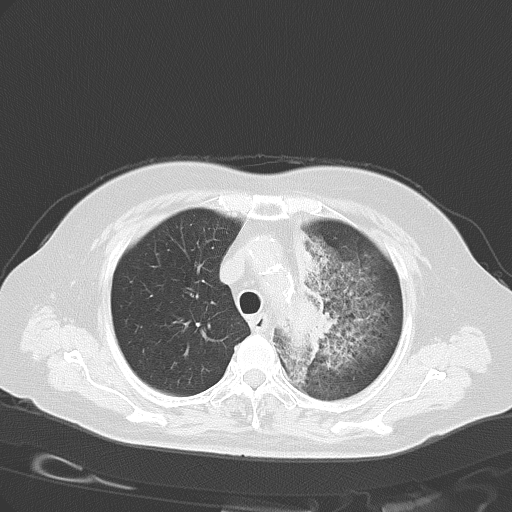
Chest CT, one axial slice; position 42 of 54 along the scan axis; reconstruction kernel B70f; 120 kVp; lung window (W 1500 / L -600 HU); 5 mm slice thickness; 512 × 512 image matrix, field of view 353 × 353 mm. Patient: female, 65 years. From the clinical record (not read from this slice): clinical TNM (as recorded): T2b N1 M0.
Structures marked on this image (rectangle marked by the reading radiologist):
- lung tumour (recorded histology: adenocarcinoma): bounding box <291,300,333,346> (left, top, right, bottom; pixels)